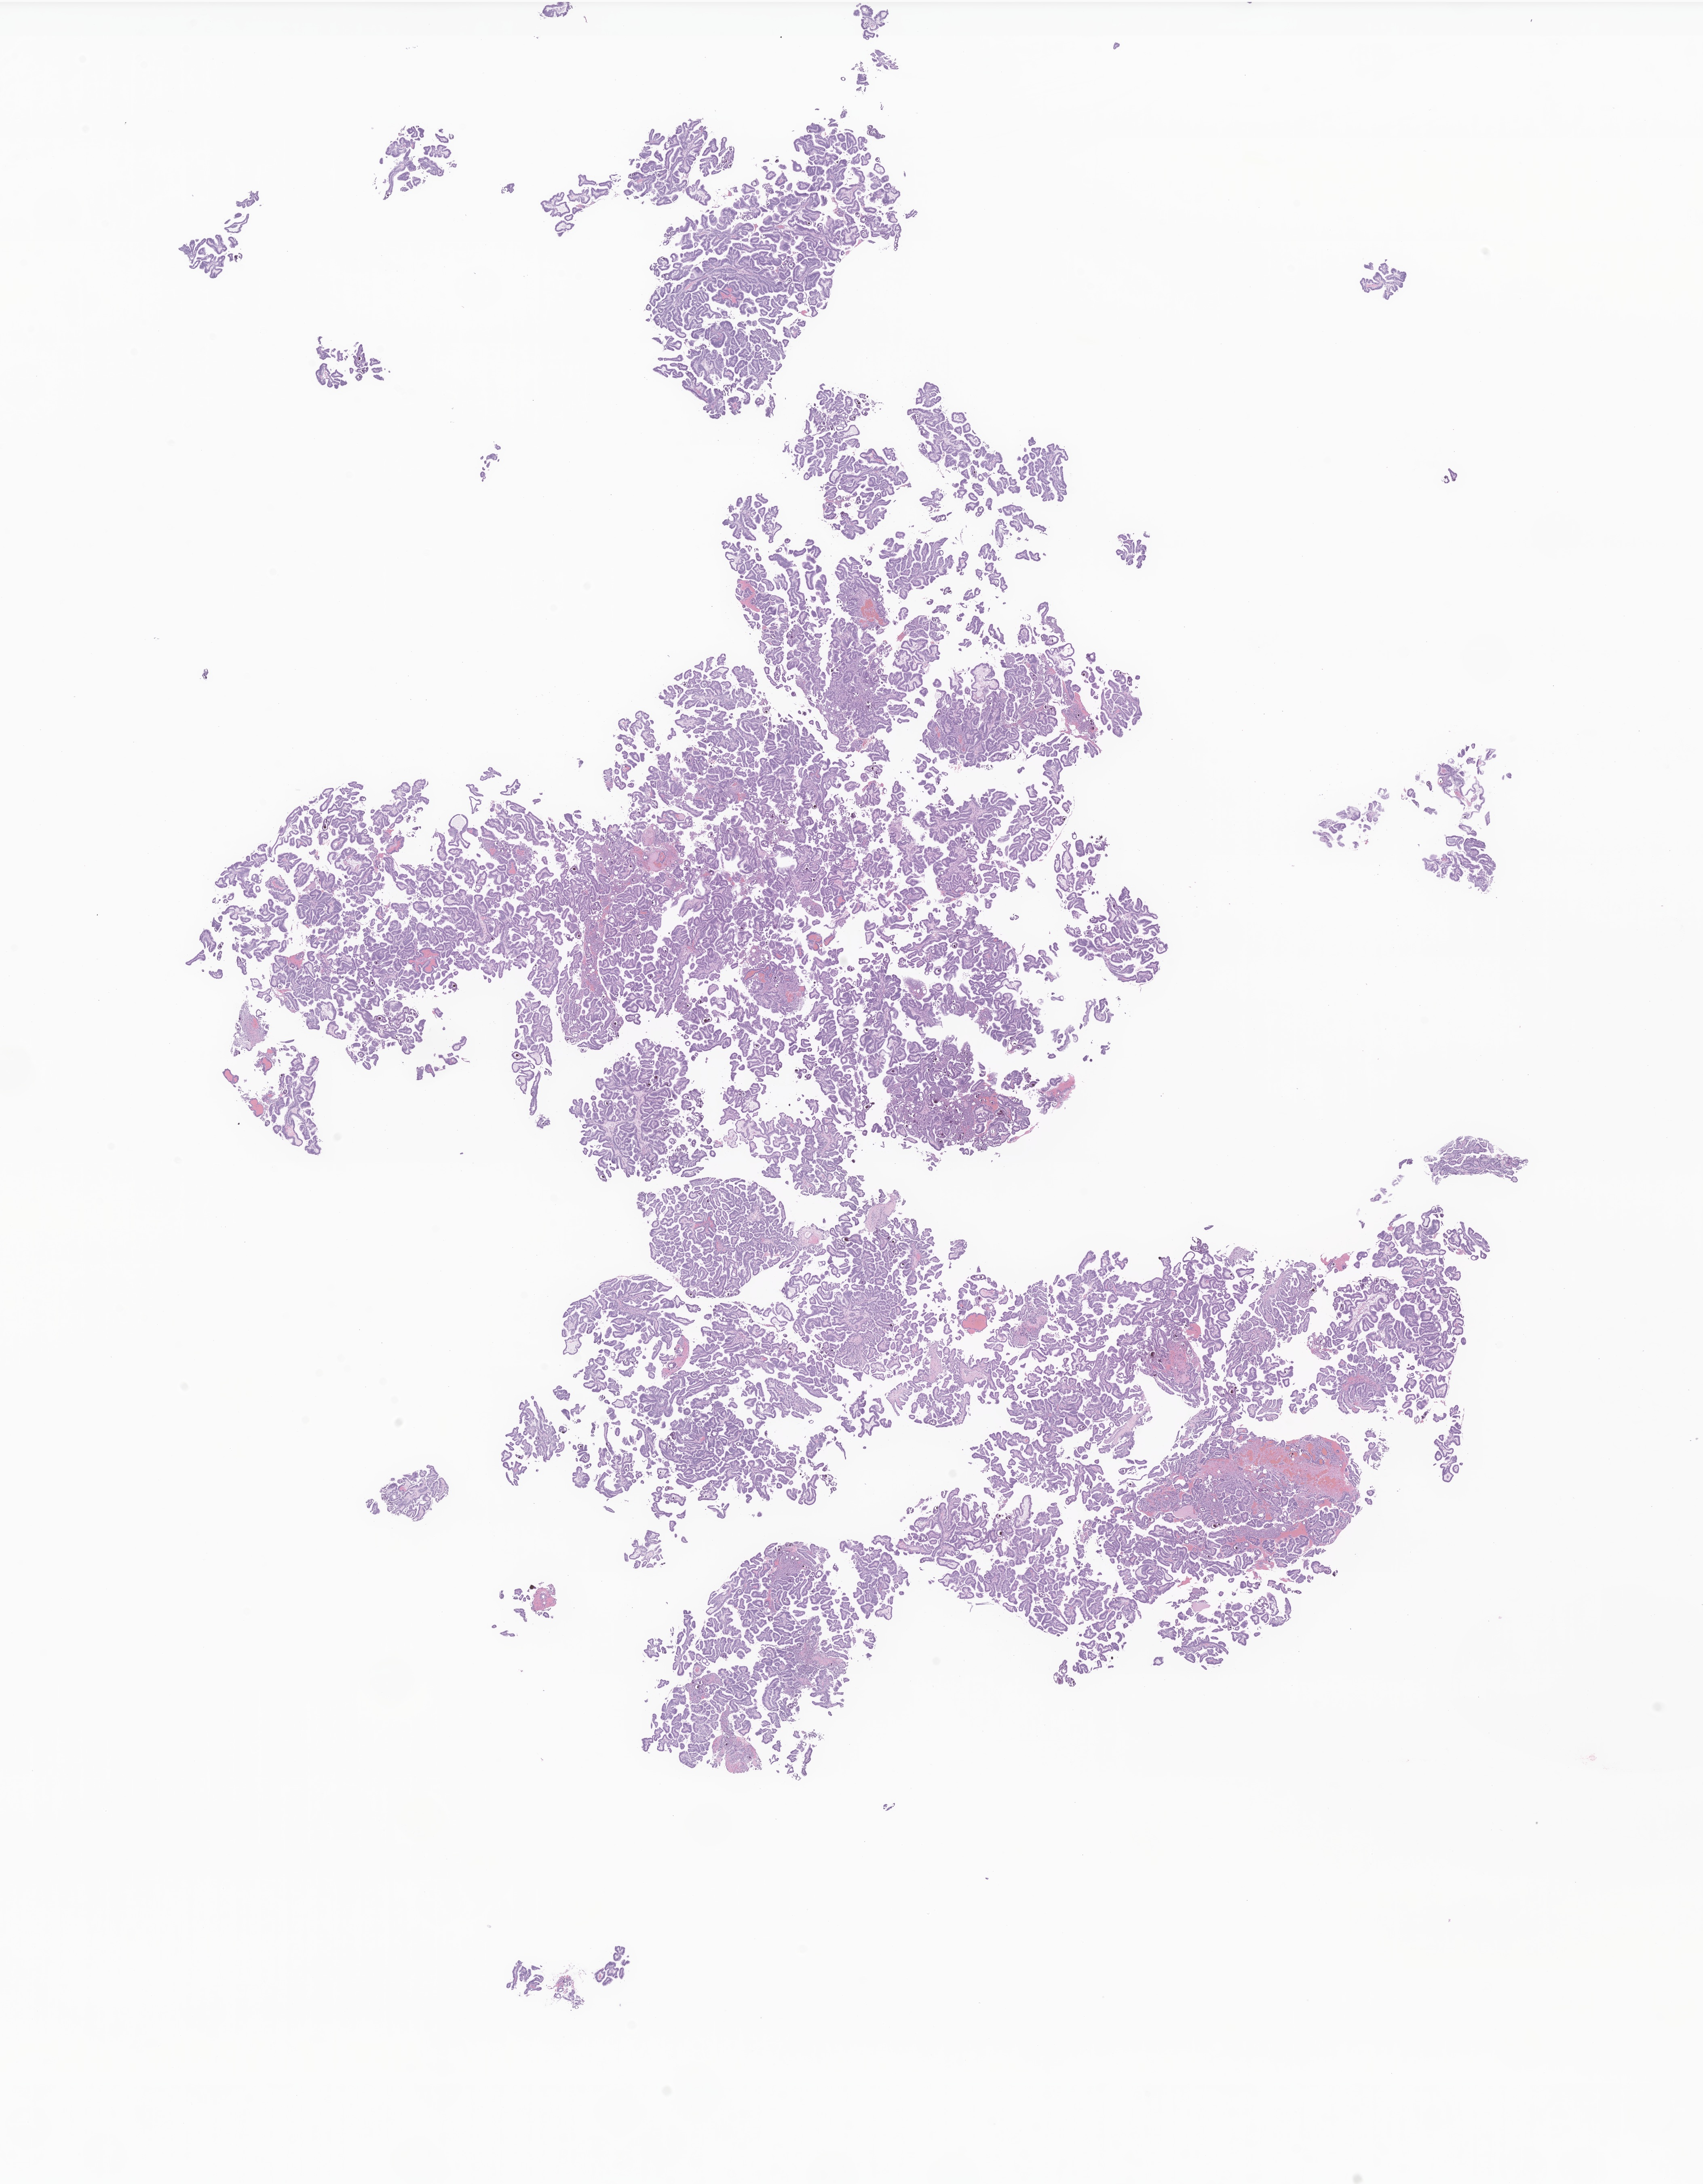
H&E whole-slide image of tumor tissue from the cerebral ventricle — whole scanned area (about 17.8 x 22.8 mm) shown as a low-resolution overview. Formalin-fixed, paraffin-embedded (FFPE) tissue. Female patient, age 639 days (about 1.7 years).
Diagnosis: Atypical choroid plexus papilloma.